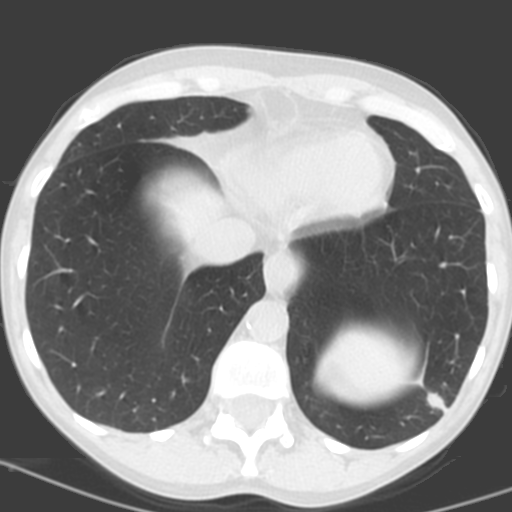
Low-dose screening chest CT, one axial slice; position 40 of 156 along the scan axis; lung window (W 1500 / L -600 HU); 3.2 mm slice thickness; 512 × 512 image matrix, field of view 262 × 262 mm.
Annotated regions visible in this slice (manually delineated by an expert):
- lesion 1 (tumor, lower lobe of left lung): bounding box (x1, y1, x2, y2) in pixels: (426, 392, 447, 412)